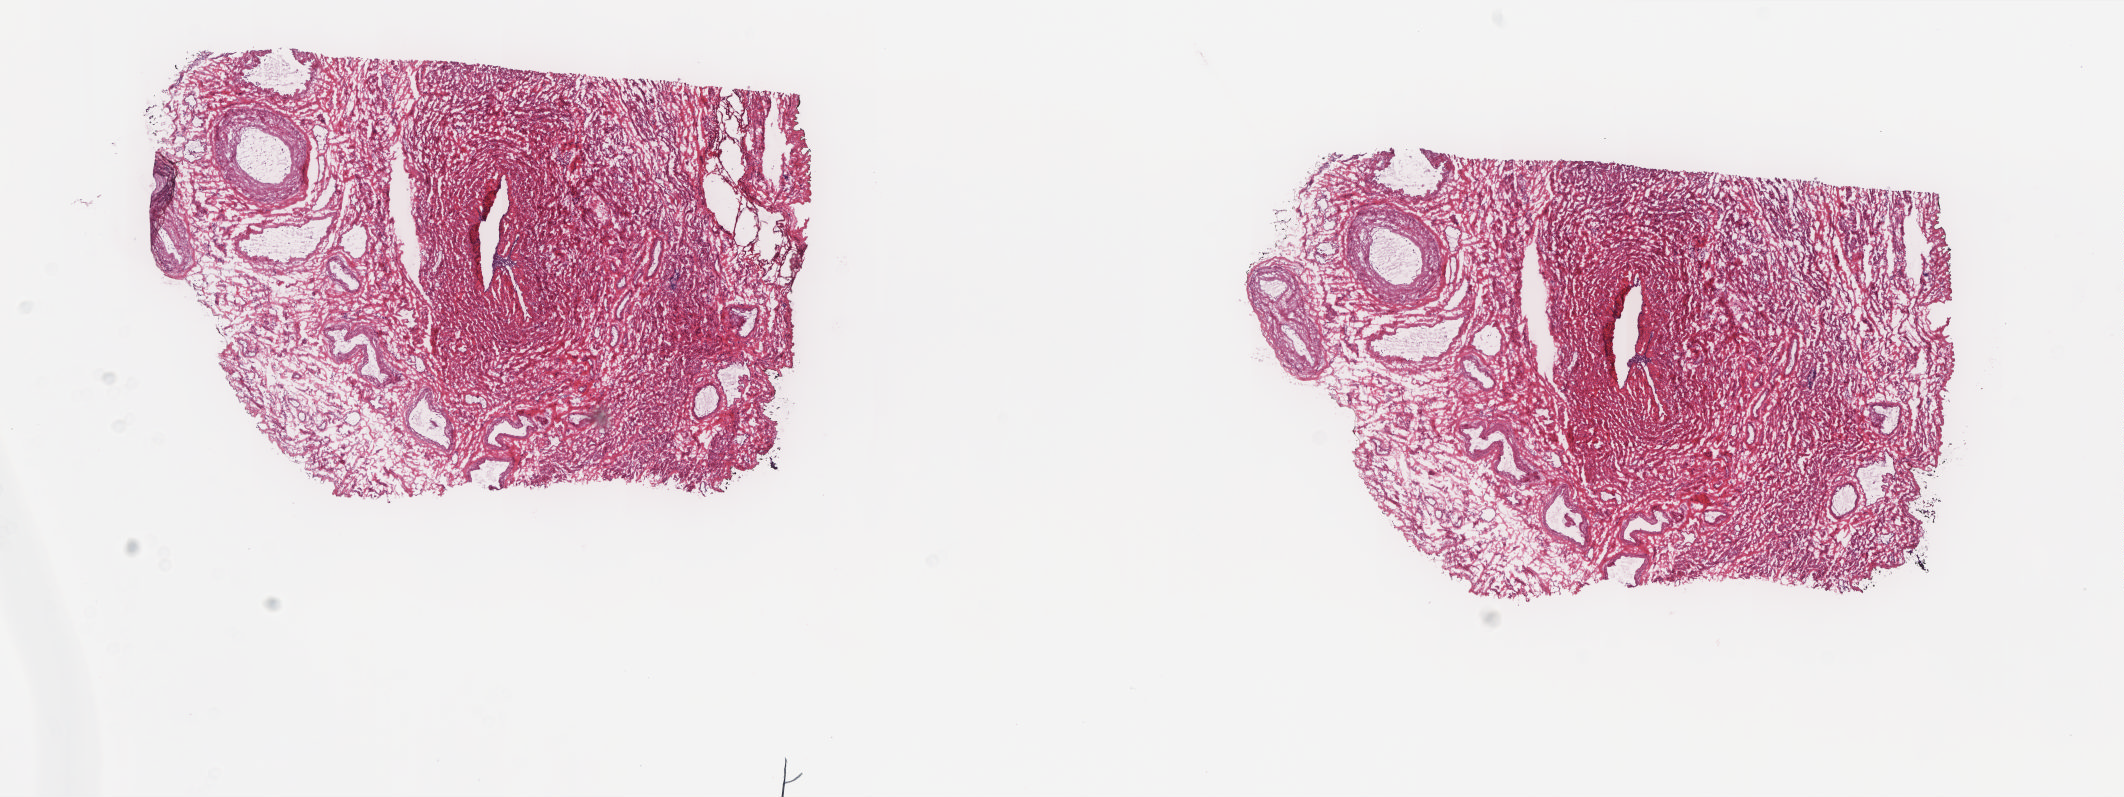
H&E-stained whole-slide image, shown as a low-resolution overview of the whole scanned area (about 17.0 x 6.4 mm, acquisition: 20x scan), frozen section from the top of the tissue portion, uterus, solid tissue normal (non-tumour tissue) sample. Female patient; age at initial diagnosis 69 years. Composition of this section per pathologist review: tumour cells 0%, tumour nuclei 0%, normal cells 100%, stromal cells 0%, necrosis 0%. Inflammatory infiltration, as recorded: lymphocyte infiltration 0%, monocyte infiltration 0%, neutrophil infiltration 0%.
- this section: solid tissue normal sample (biorepository sample class)
- patient diagnosis: Endometrioid adenocarcinoma, NOS (endometrium)